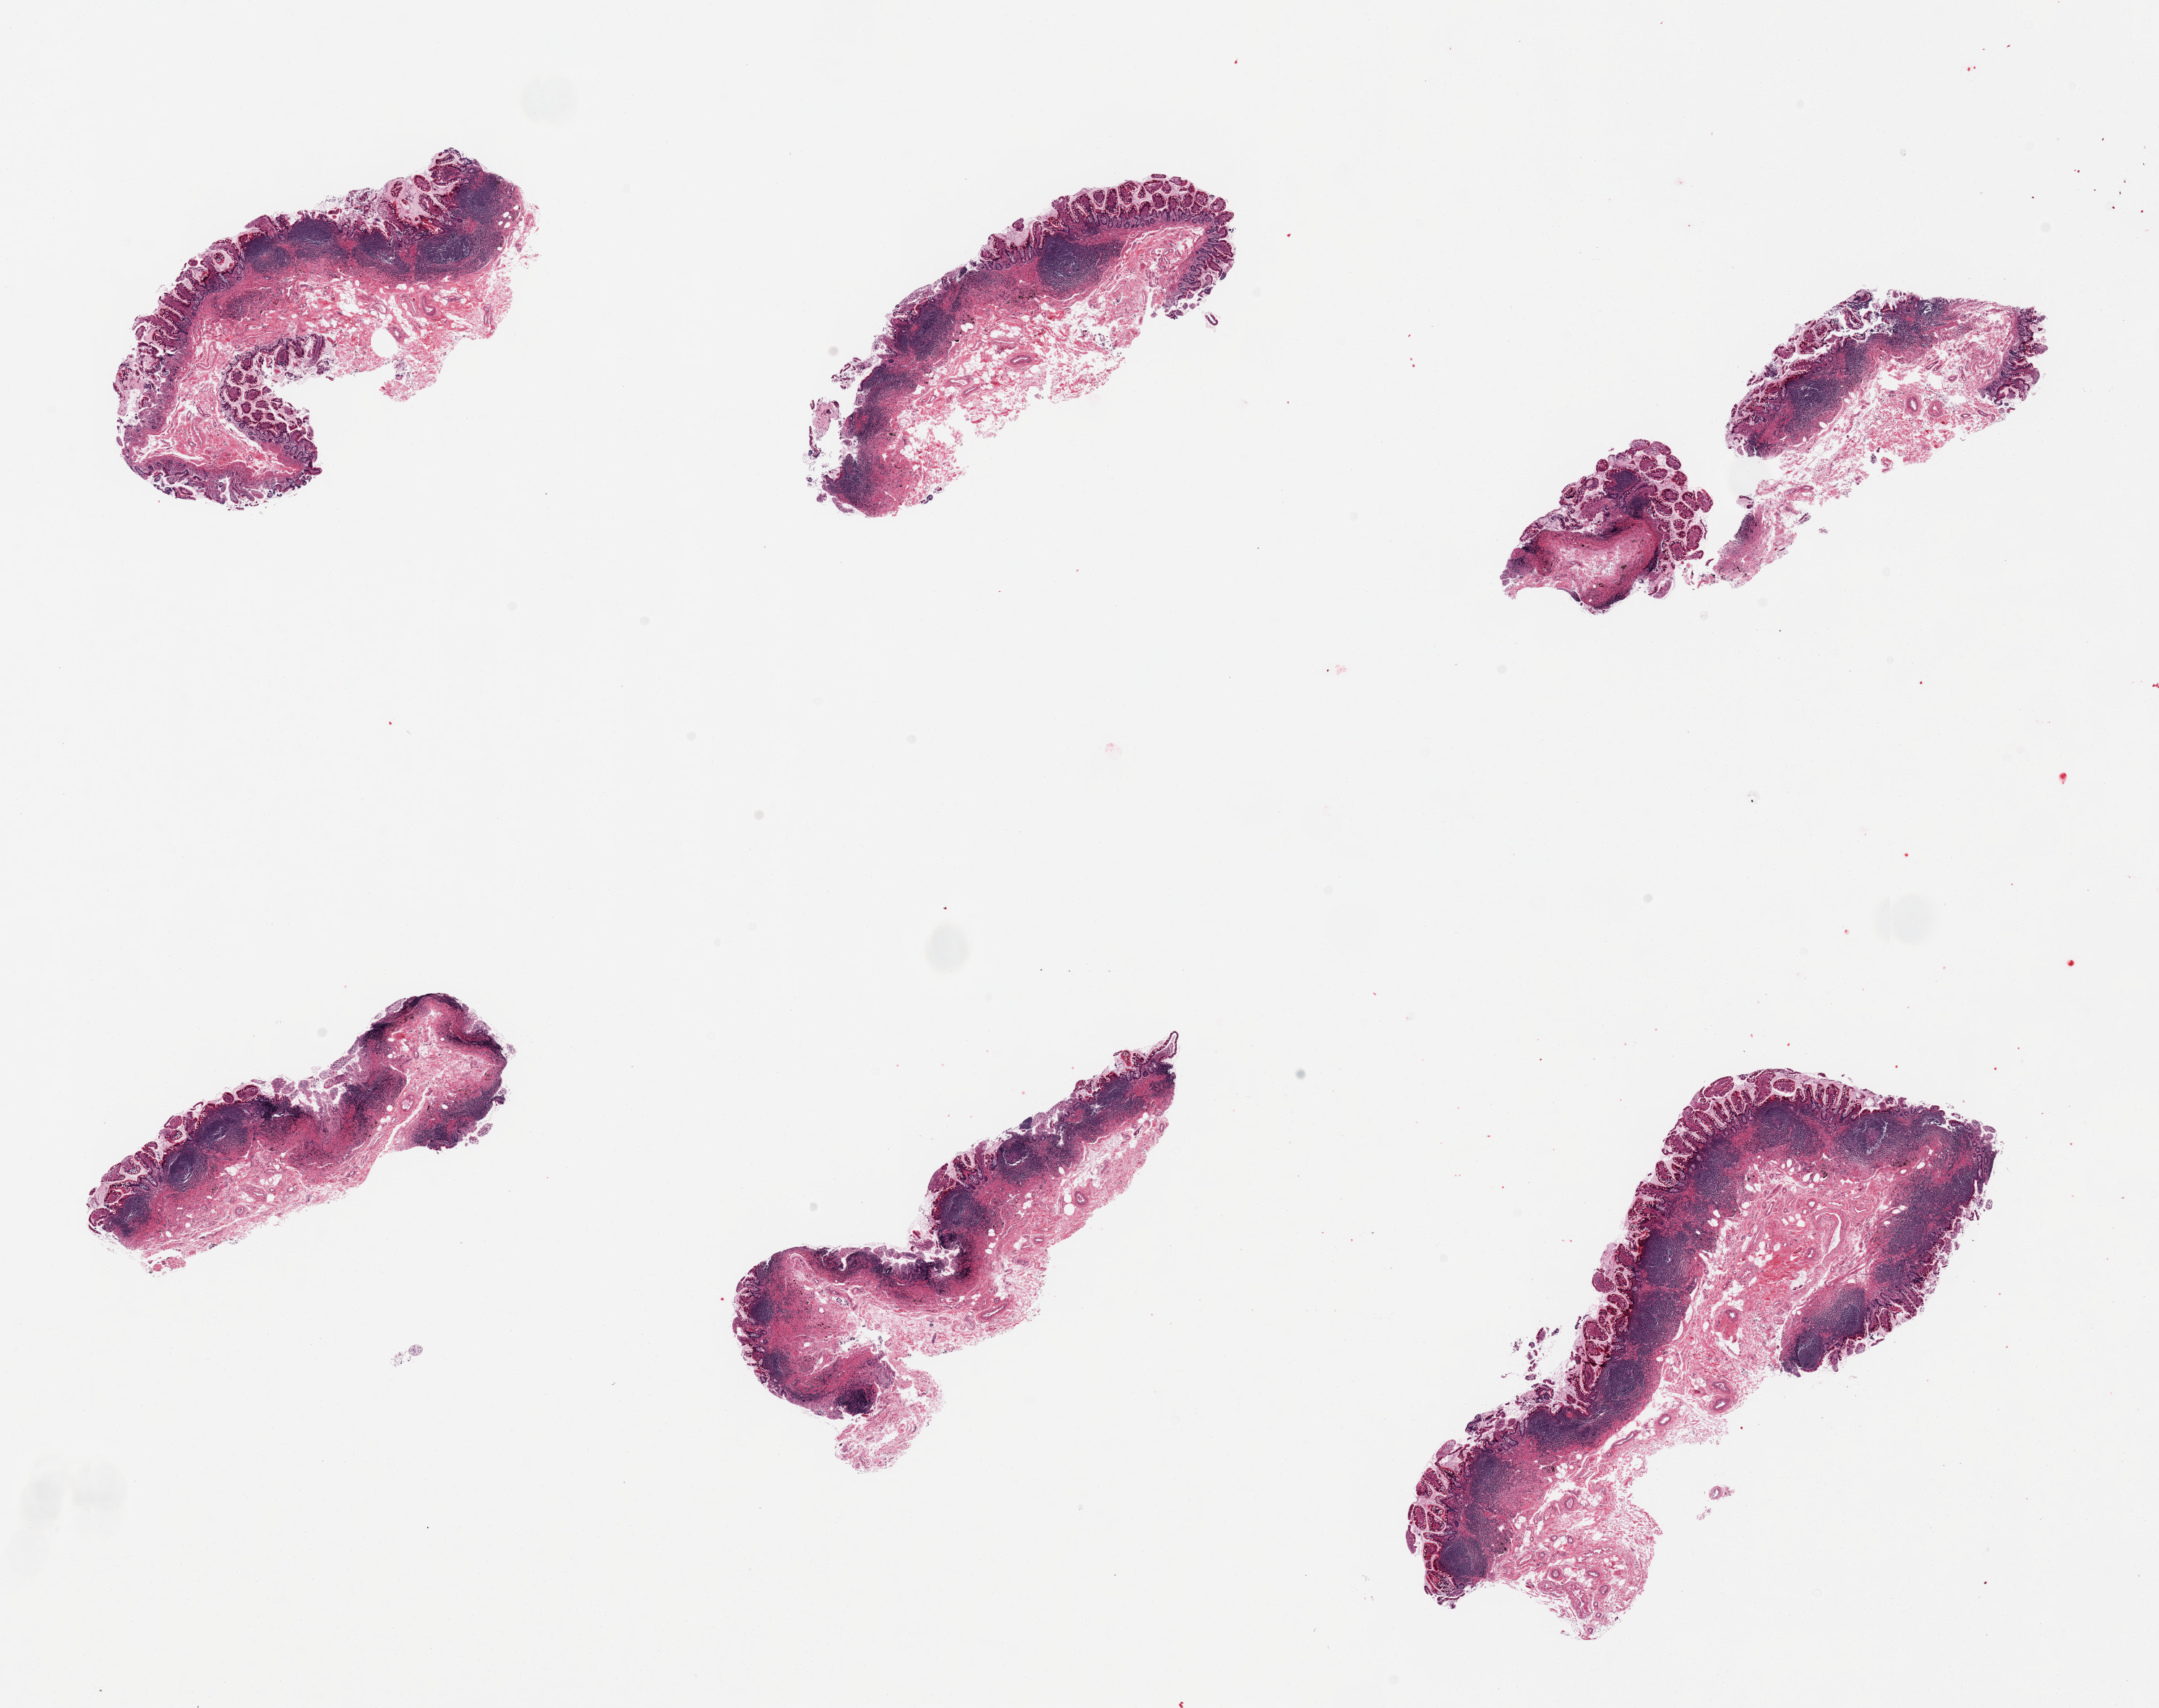
Haematoxylin and eosin whole-slide image — shown as a low-resolution overview of the whole scanned area (about 23.6 x 18.7 mm, slide scanned at 20x); PAXgene-fixed, paraffin-embedded tissue; target tissue: ileum; tissue donor sample. Female donor.
Review note (as recorded): 6 pieces, well-preserved, lymphoid aggregares are ~20% total, good specimen.